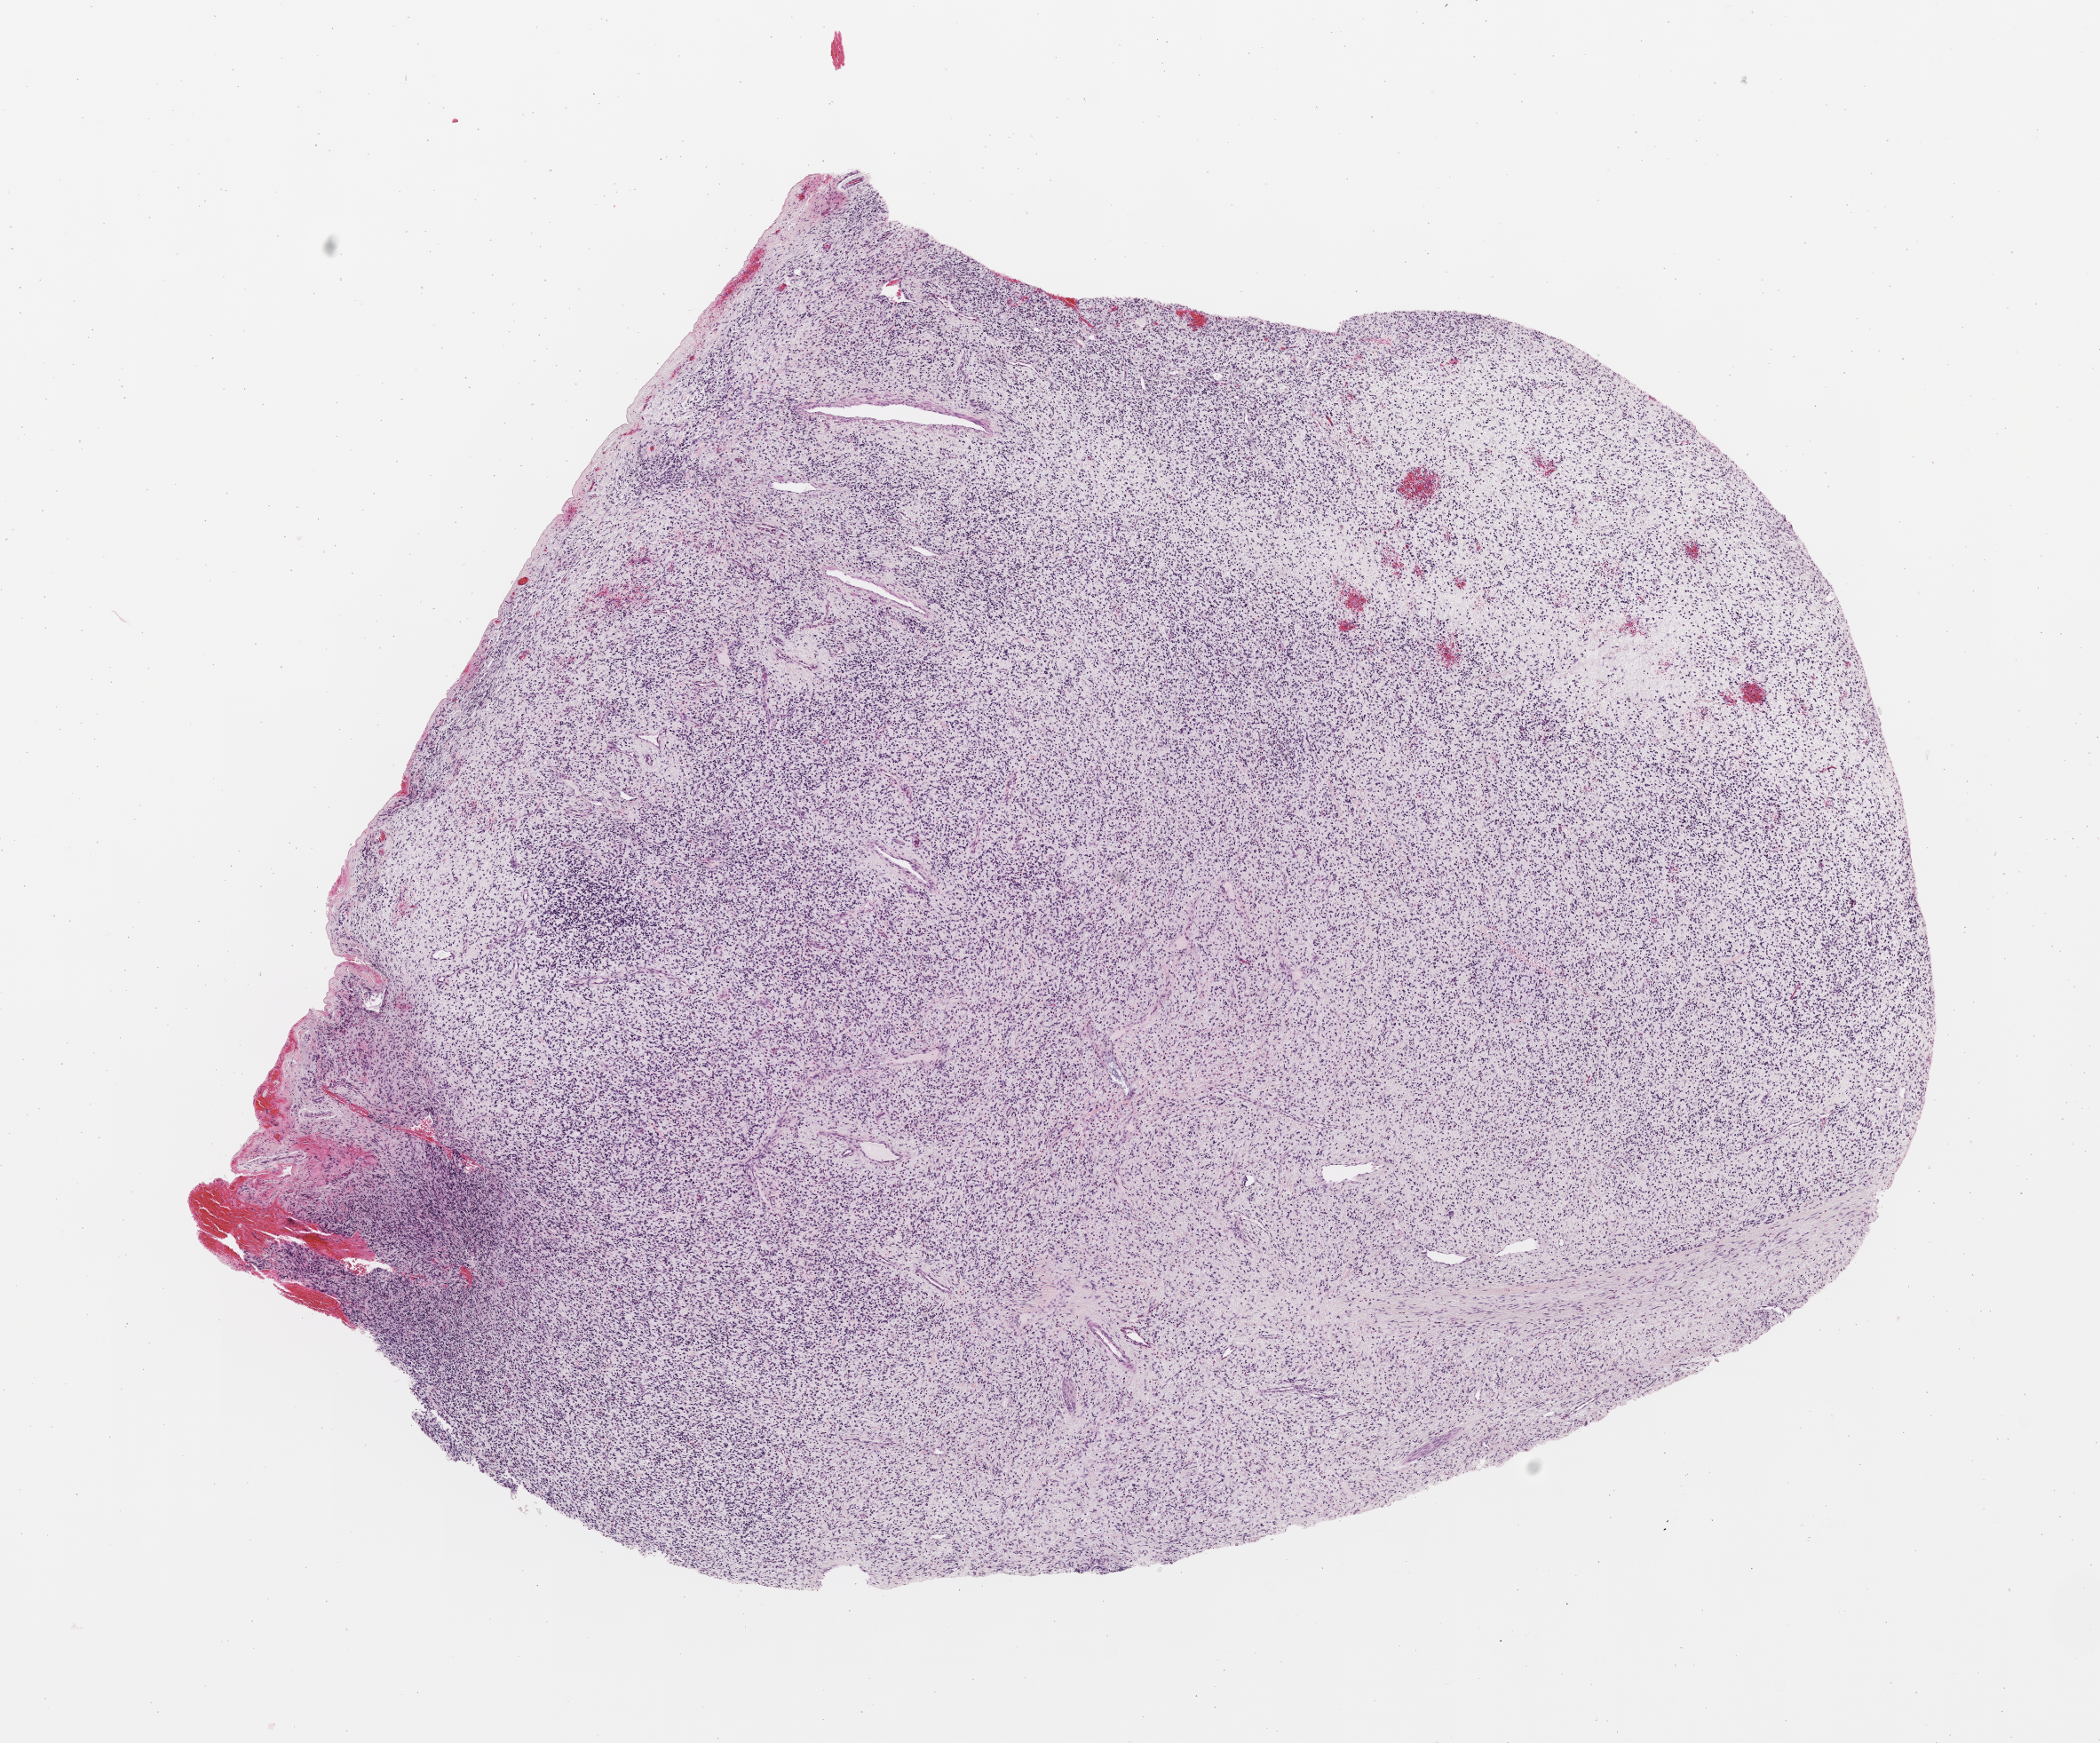
Haematoxylin and eosin whole-slide image of tumor tissue, whole scanned area (about 9.6 x 7.9 mm) shown as a low-resolution overview, formalin-fixed paraffin-embedded section, site: bile duct/bilary tract. Patient: male, age 2.7 years at diagnosis.
- stage (as recorded): 1
- diagnosis: rhabdomyosarcoma; histological classification: embryonal rhabdomyosarcoma